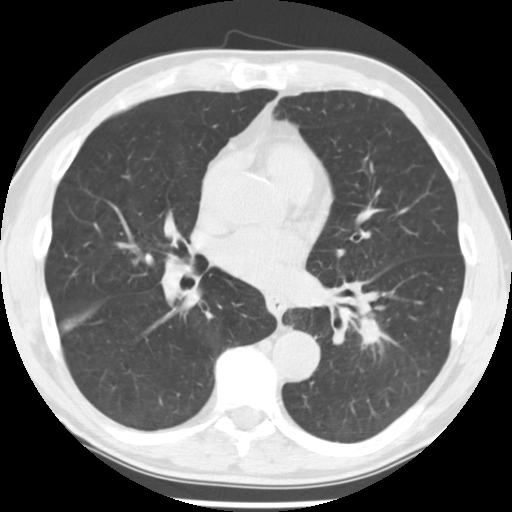
Low-dose screening chest CT, axial slice; third screening round (two years after baseline); lung window (W 1500 / L -600 HU); 2.5 mm slice thickness; standard (soft-tissue) reconstruction kernel (STANDARD). Male, age 64 years at enrolment. Current smoker at enrolment.
- Expert reader's lesion annotation, bounding box [x1, y1, x2, y2] px = [351, 317, 390, 349].
- No non-calcified nodule or mass ≥4 mm was recorded by the screening reader at this exam.
- Official screen result: negative screen, no significant abnormalities.